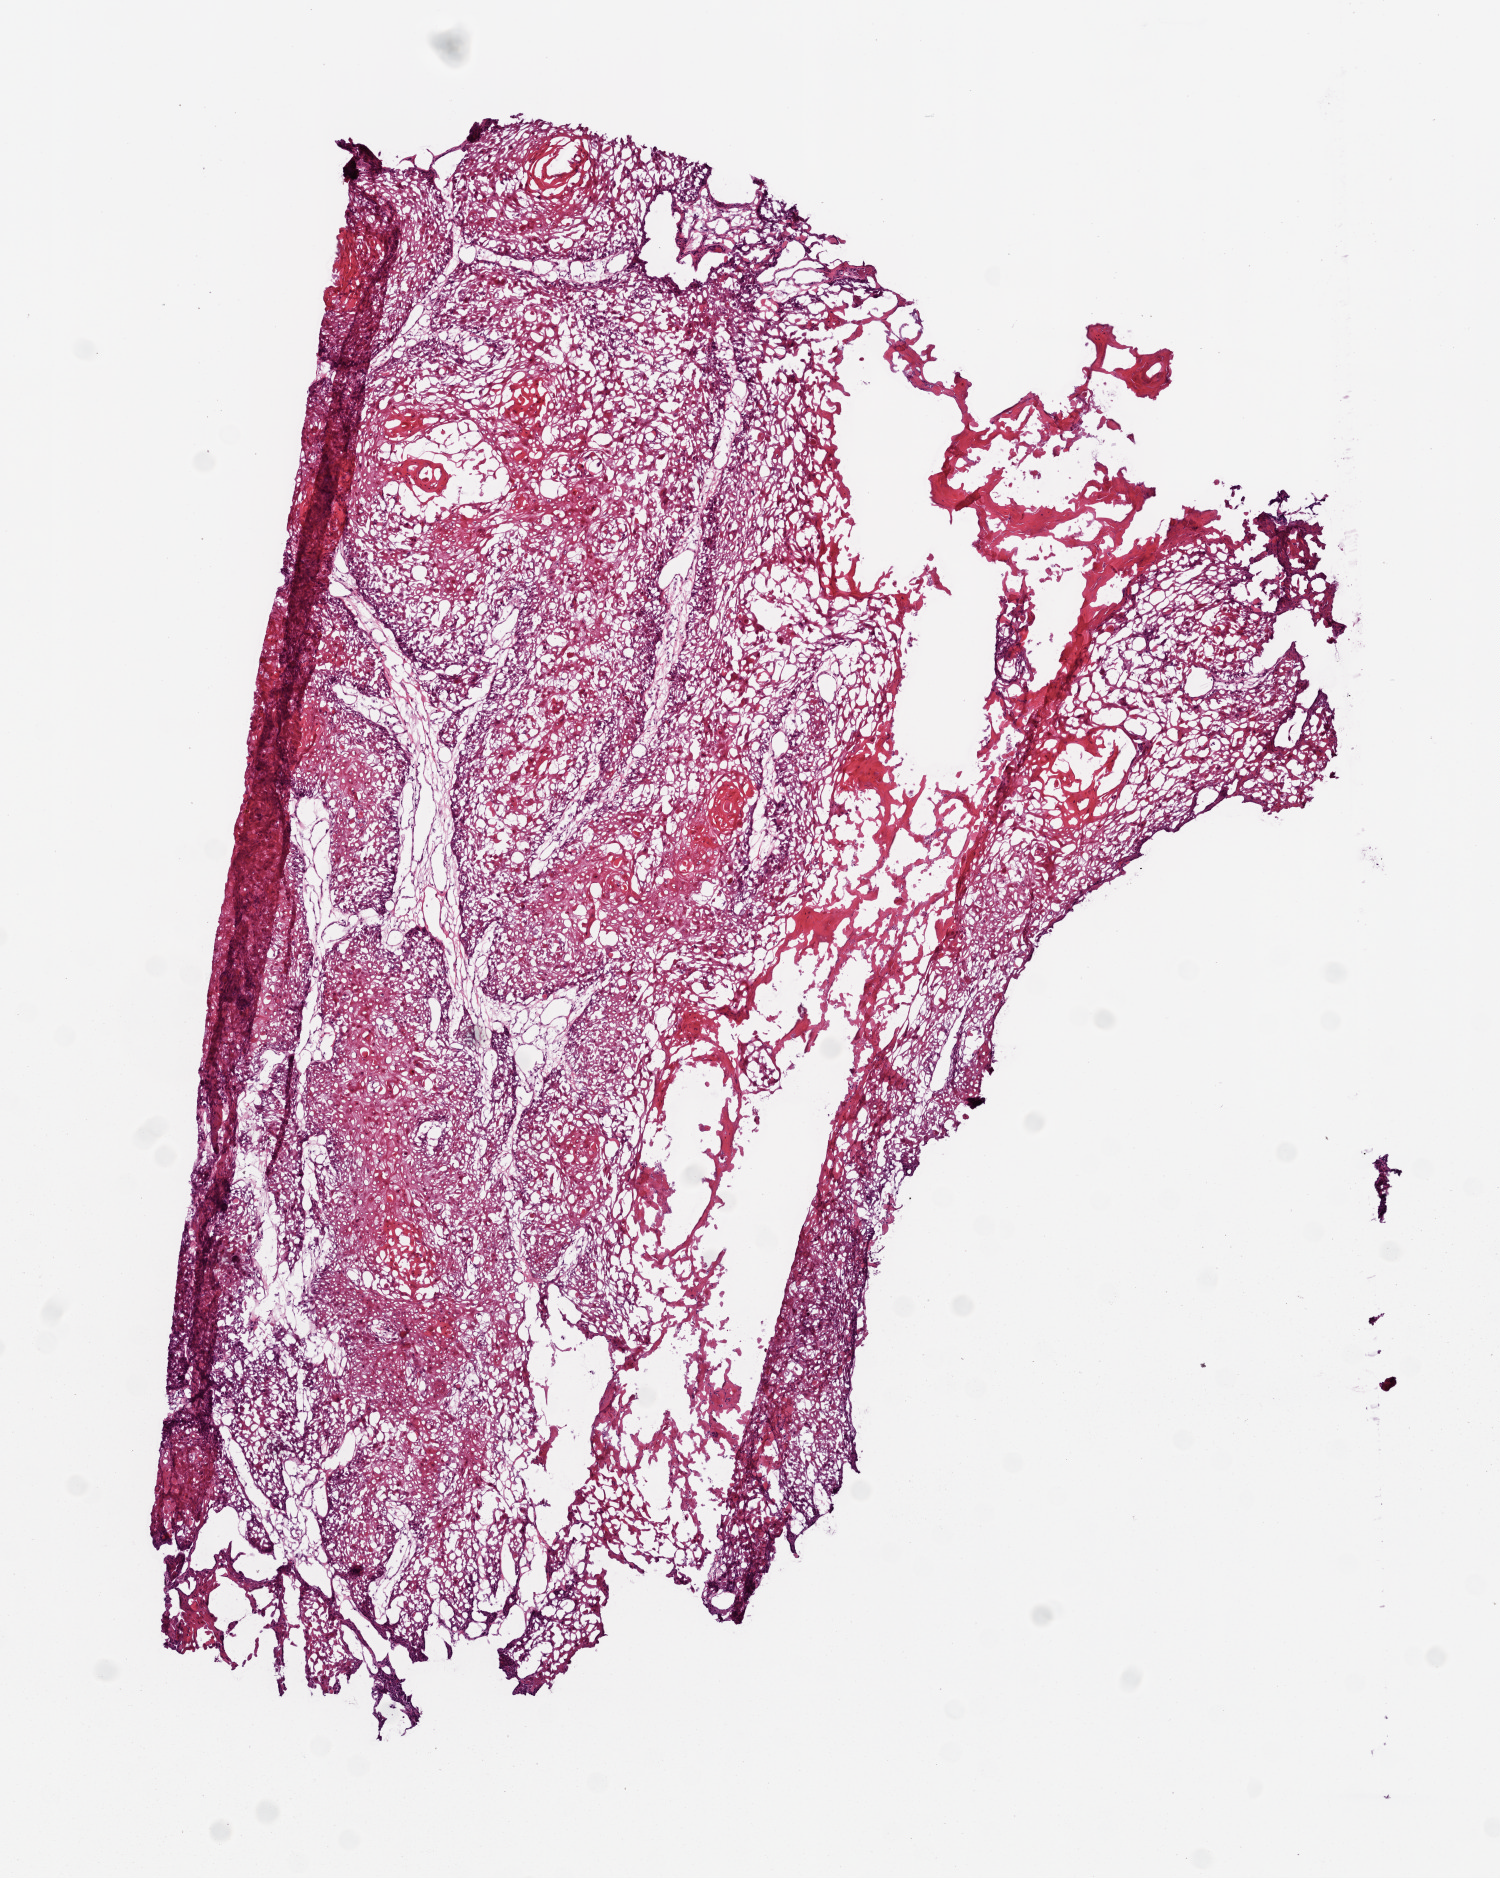
H&E-stained whole-slide image — a low-resolution overview of the entire scanned area, about 6.0 x 7.5 mm (slide scanned at 20x); frozen section; head and neck, primary tumour sample. Male patient; age at initial diagnosis 38 years. Histologic grade: G2 (moderately differentiated). Slide review estimates, as recorded: tumour cells 95%, tumour nuclei 90%, normal cells 0%, stromal cells 5%, necrosis 0%.
TNM: T2 N3. AJCC pathologic stage: IVB (6th edition). Pathologic diagnosis: Squamous cell carcinoma, NOS (tonsil, NOS). Lymph nodes positive (case pathology): 1 of 9 examined.